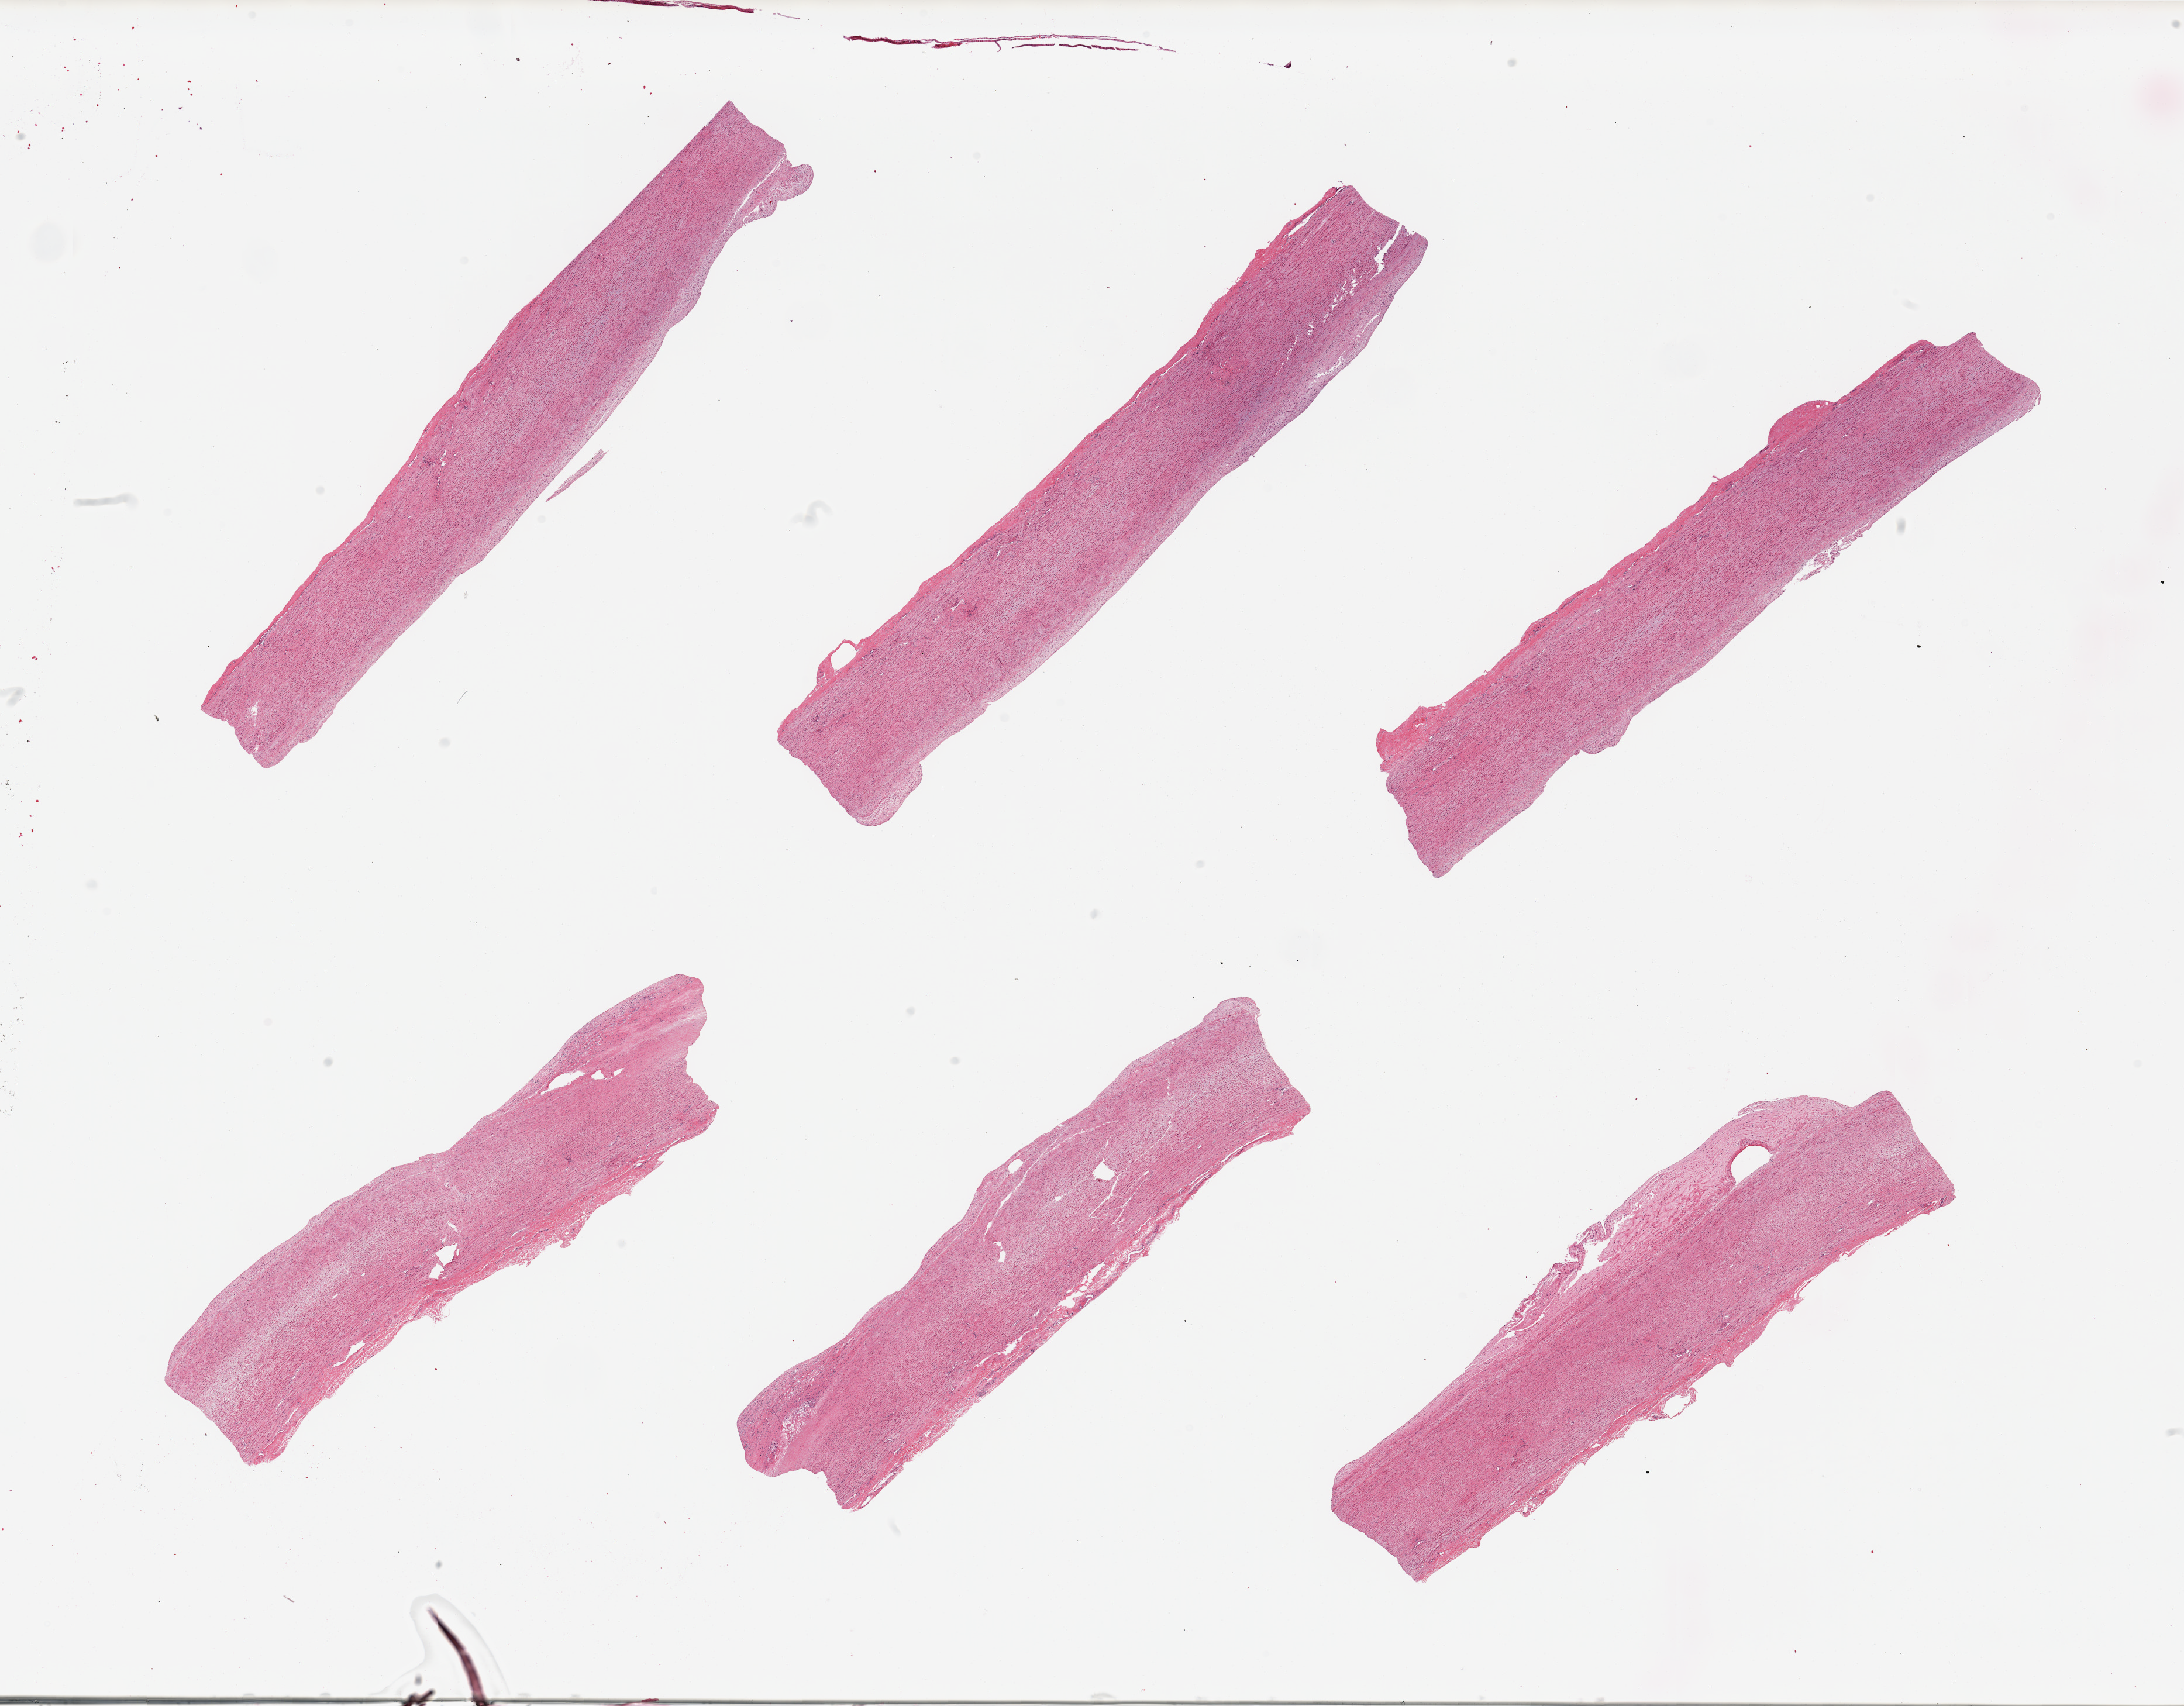
Digitized H&E-stained section, shown as a low-resolution overview of the whole scanned area (about 29.5 x 23.1 mm, from a 20x scan), PAXgene-fixed, paraffin-embedded tissue, section of aorta (target tissue), tissue donor sample. Donor: male.
* review note (as recorded): 6 pieces; mild plaques; well trimmed